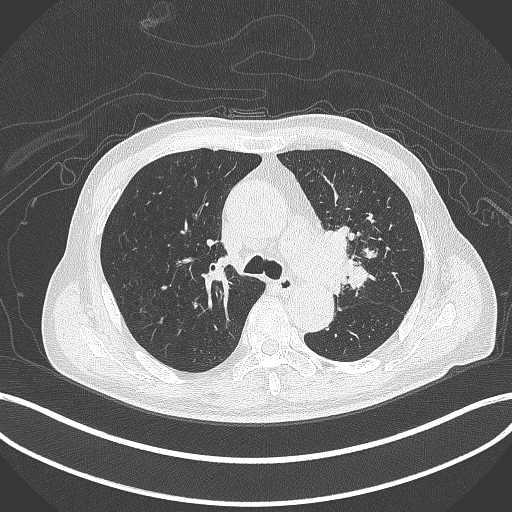
Chest CT, one axial slice. Slice 288 of 417 in the series (ordered by position). 120 kVp. Lung window (W 1500 / L -600 HU). 512 × 512 image matrix, field of view 400 × 400 mm. Male patient, age 77 years. Case-level facts recorded for this patient, not image findings: clinical TNM (as recorded): T3 N1 M0.
Outlined on this slice (bounding box drawn by a radiologist):
- lung tumour (recorded histology: adenocarcinoma): bounding box (x1, y1, x2, y2) in pixels: (314, 224, 361, 291)